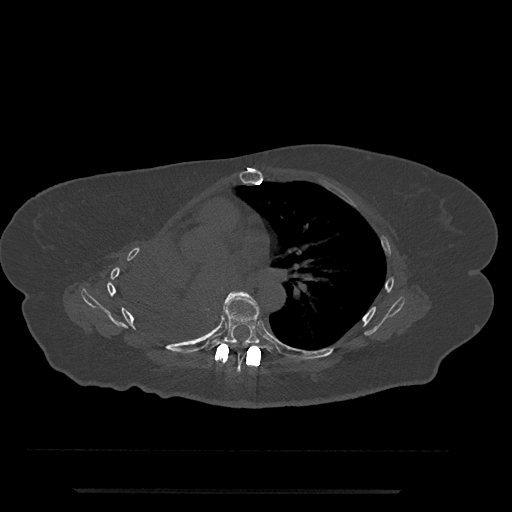
CT including the spine, one axial slice; position 464 of 797 along the scan axis; reconstruction kernel Br40s/3; 120 kVp; bone window (W 1800 / L 400 HU); 0.5 mm slice thickness; 512 × 512 image matrix, field of view 440 × 440 mm. Female patient, age 51 years. Case-level facts recorded for this patient, not image findings: primary cancer: neuro; vertebrae with lytic lesions (as recorded): T8.
Structures marked on this image (semi-automatically segmented with operator editing):
- T6 vertebra: box from (x=226, y=350) to (x=245, y=372) px
- T7 vertebra: (x=204, y=292)–(x=277, y=356)